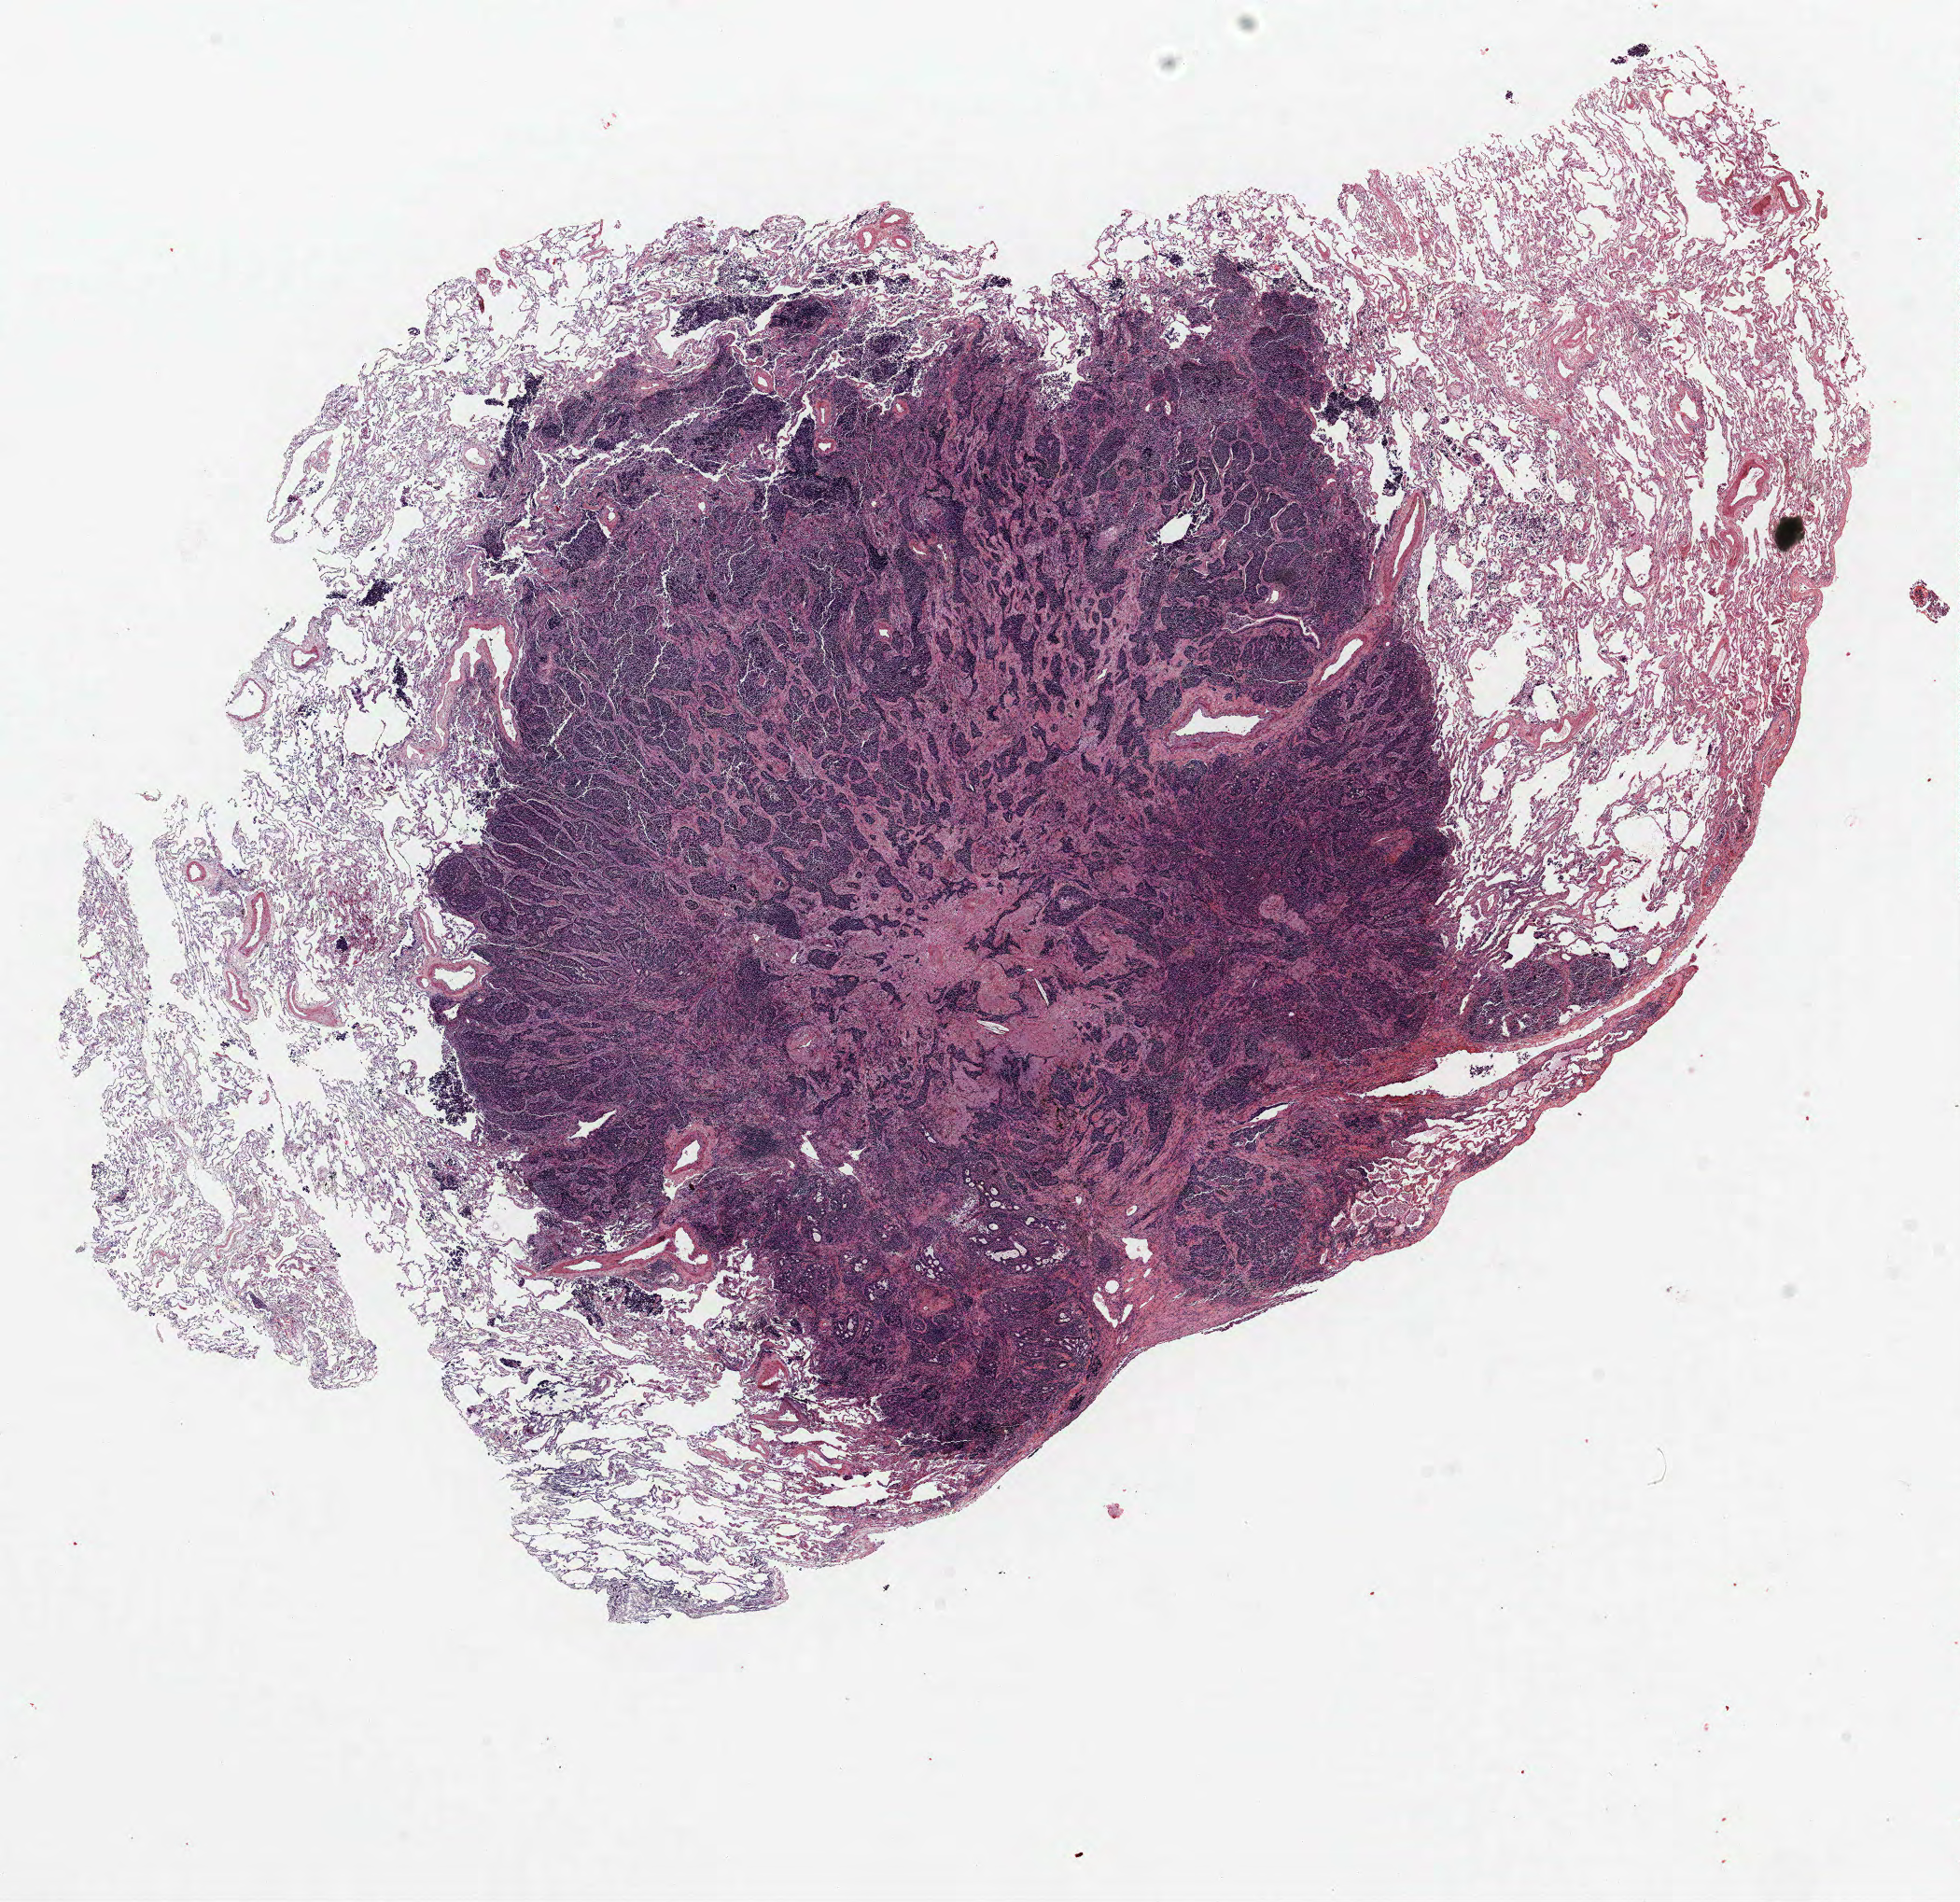
Whole-slide histology image, H&E, low-resolution overview of the scanned area, about 16.8 x 16.3 mm. FFPE section. Lung. Male patient, aged 64 at enrolment. Grade: poorly differentiated (G3).
• tumour size (pathology): 11 mm
• participant's lung-cancer diagnosis: Adenocarcinoma, NOS
• stage (AJCC 6th edition): IA
• primary tumour location (clinical record): right upper lobe